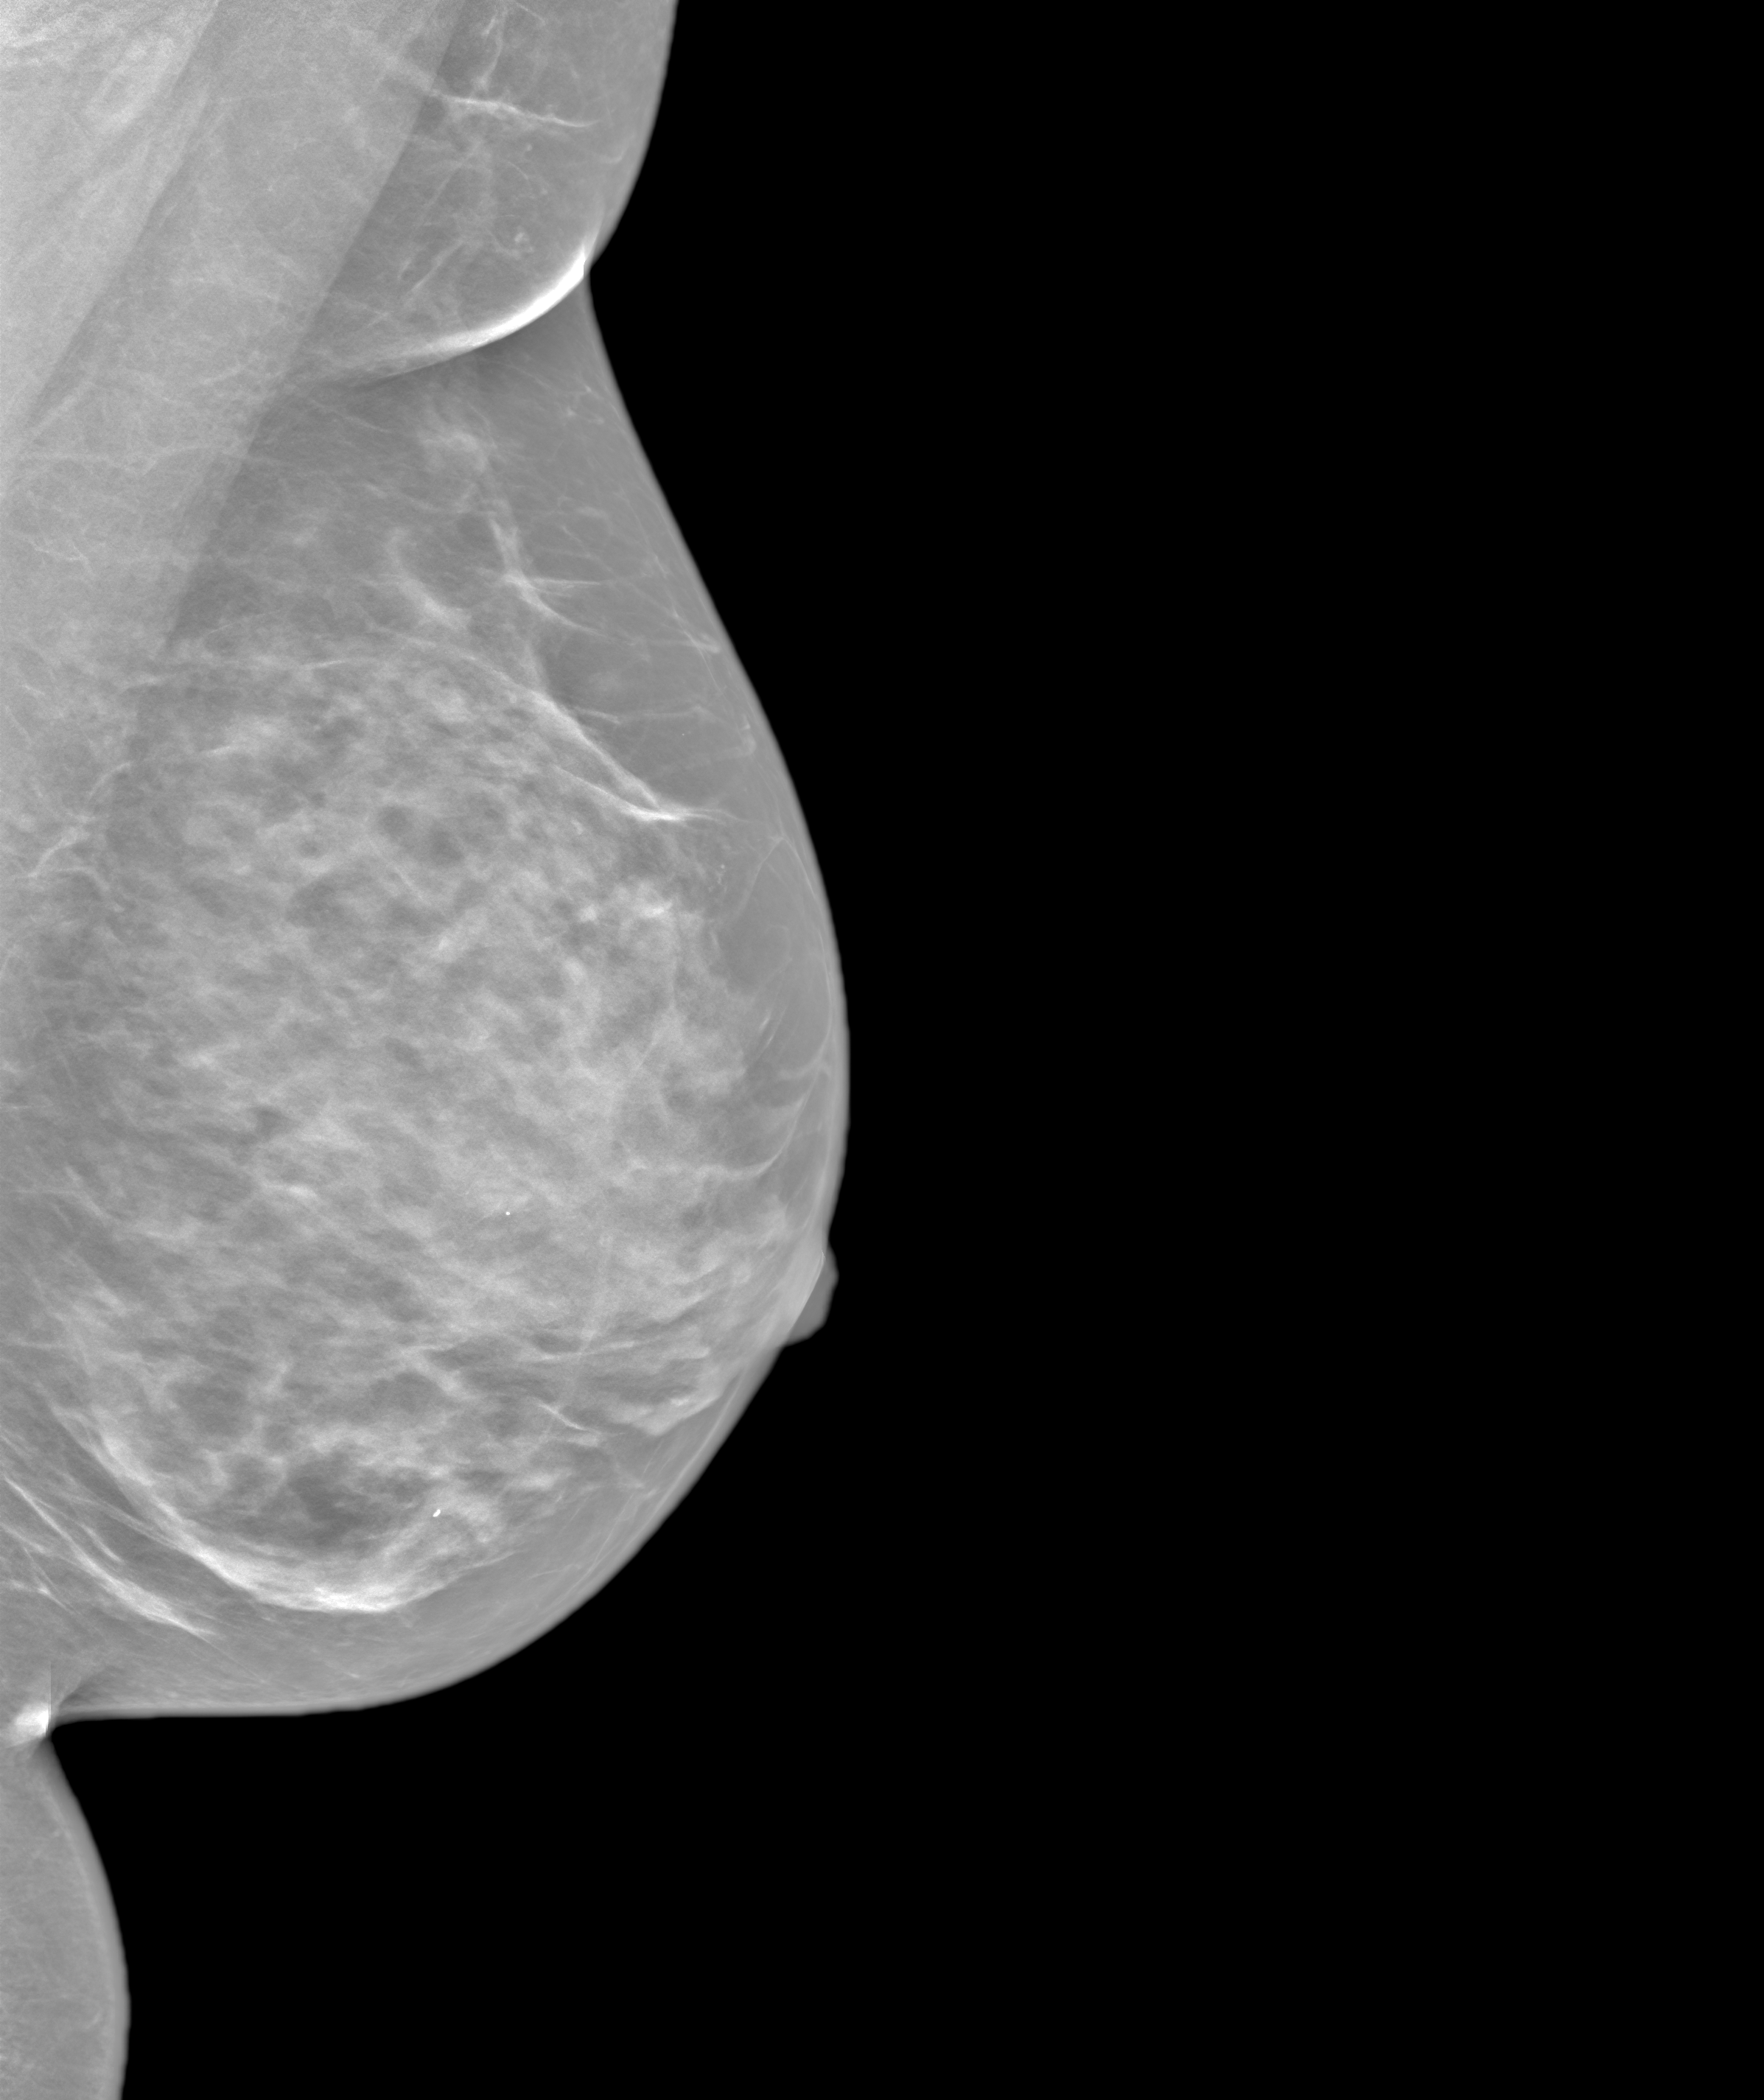
Synthetic 2-D view generated from a tomosynthesis acquisition (not an FFDM exposure), left breast, mediolateral oblique (MLO) view, annual screening mammography examination, system: SenoIris_1SP1.1(421). Patient aged 42 years (female).
Breast density at the screening exam (both breasts): extremely dense (BI-RADS density category d). Final BI-RADS assessment for this screening round (tomosynthesis exam, both breasts): category 1. Recall: no recall after this screen.